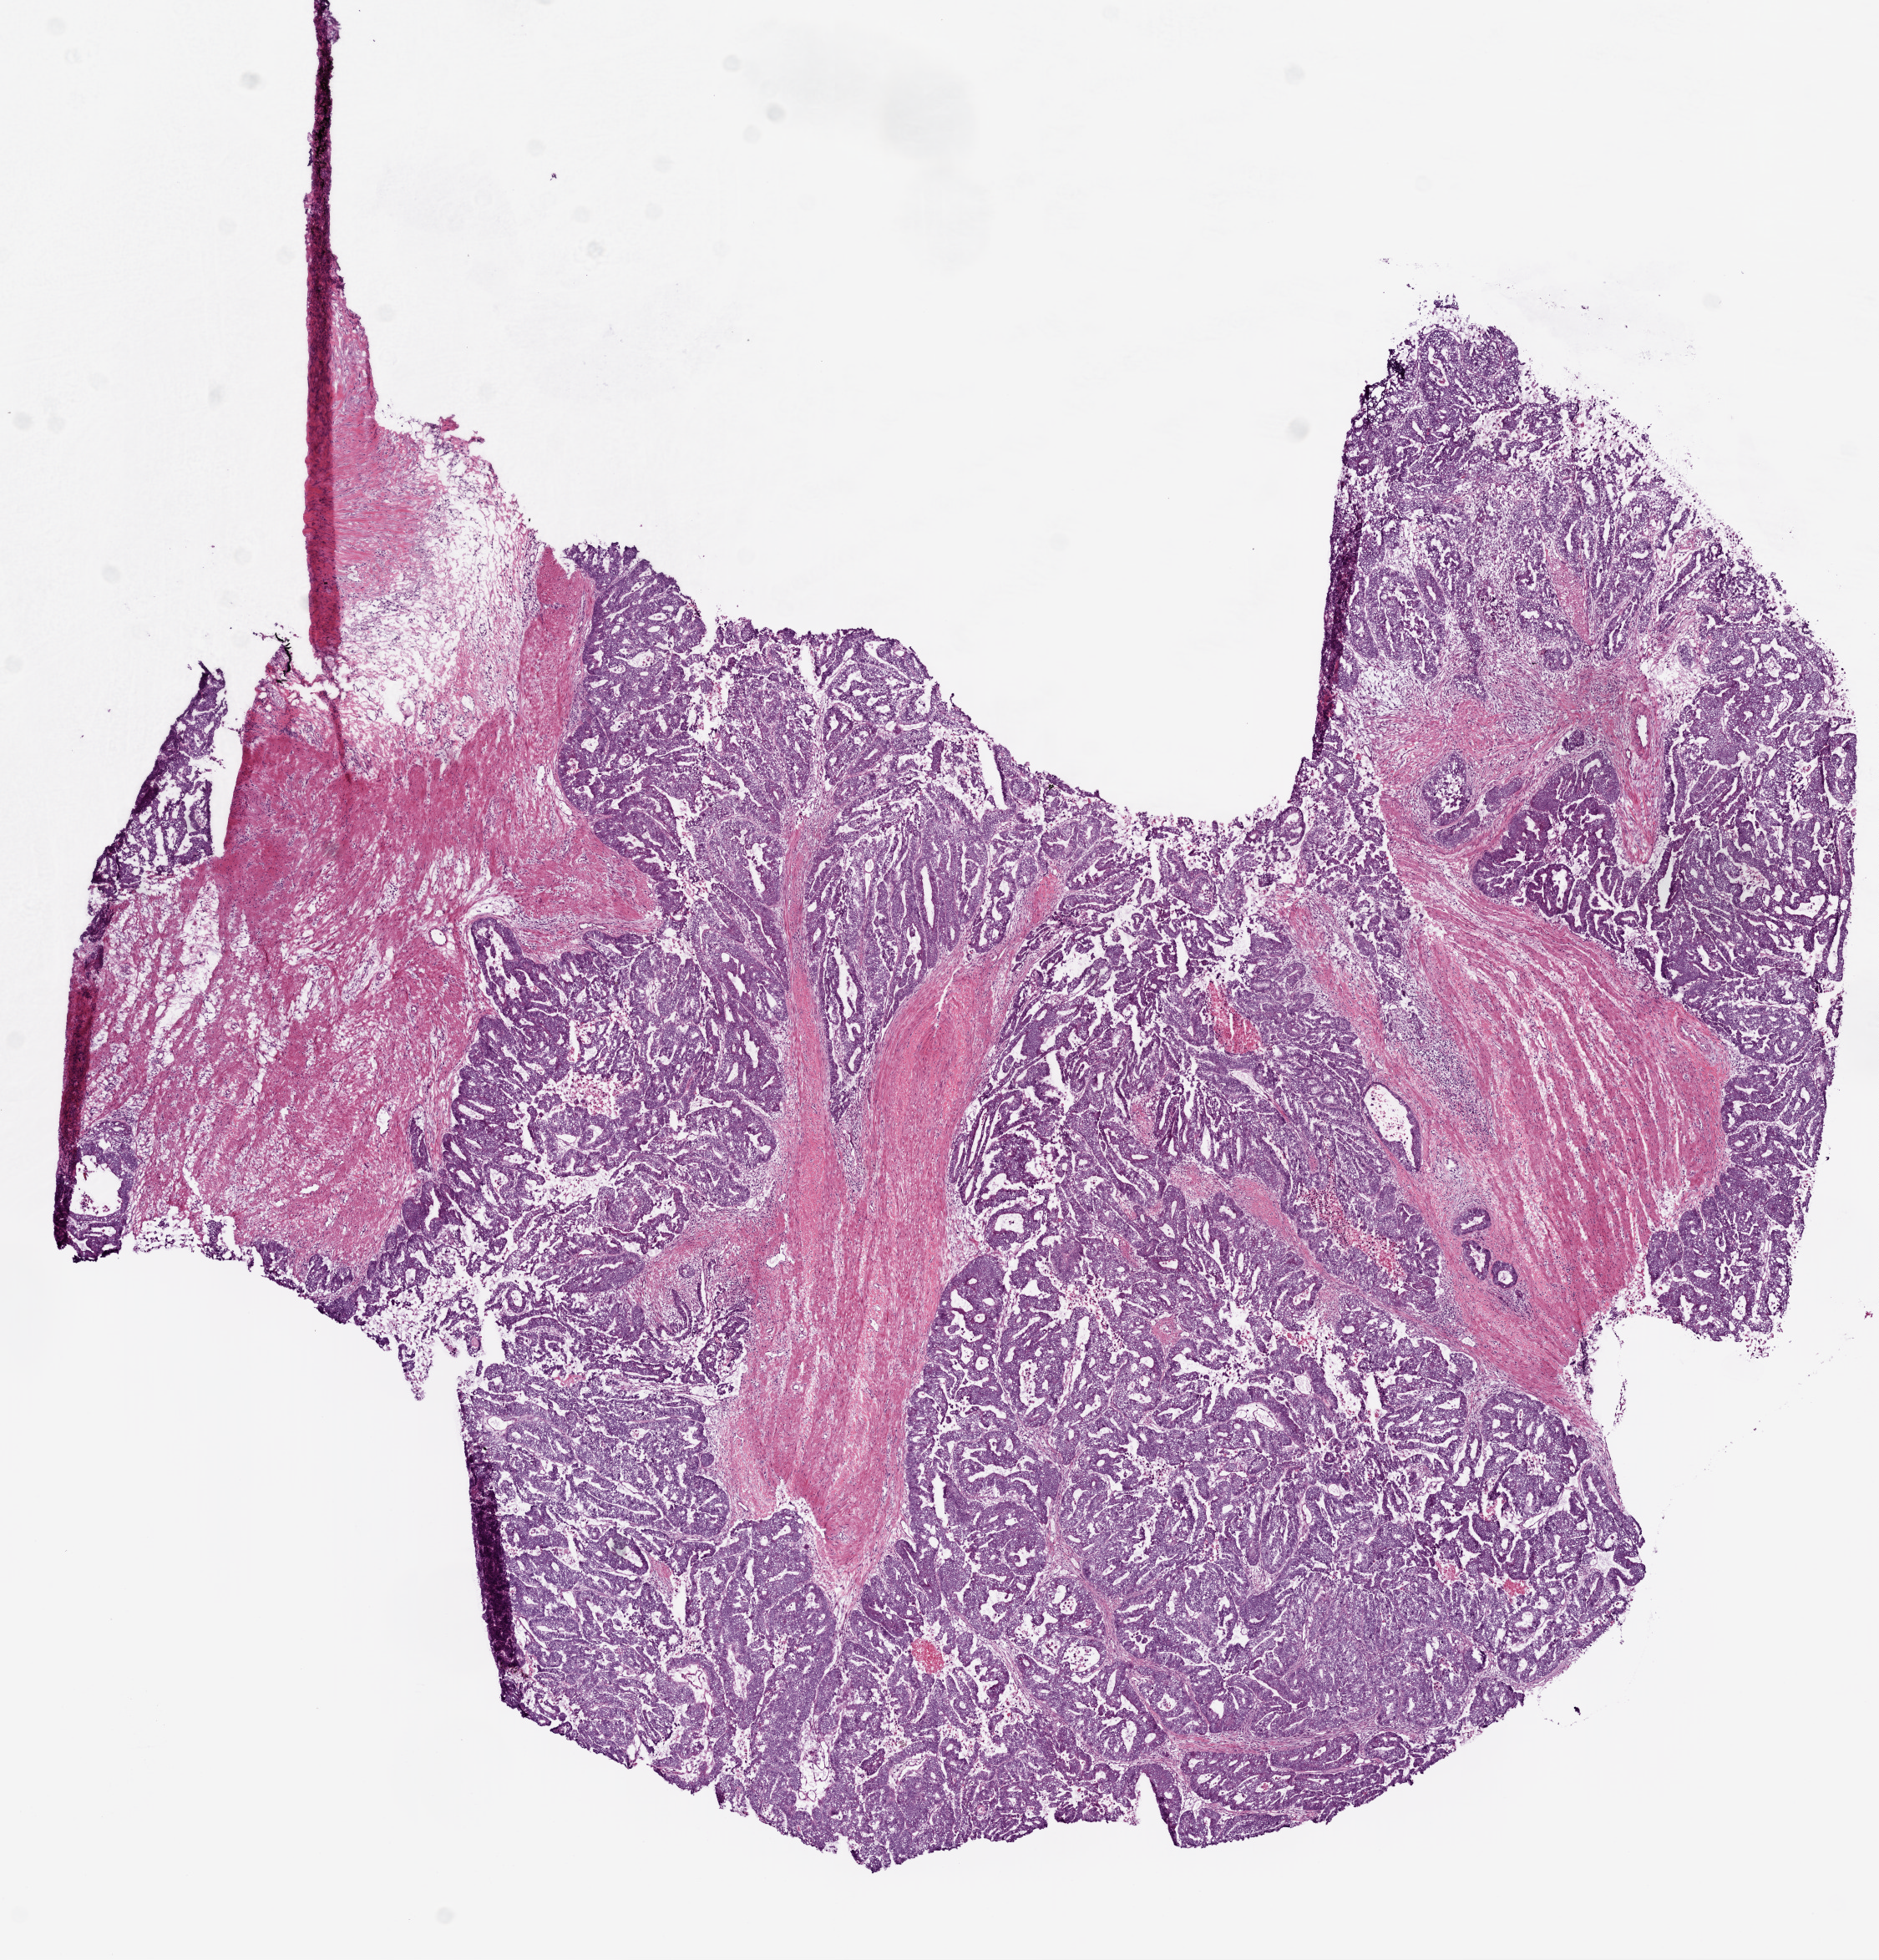
Hematoxylin and eosin (H&E) stained whole-slide image — low-resolution overview of the scanned area, about 9.0 x 9.4 mm. Frozen section from the bottom of the tissue portion. Primary tumour sample from the colon. Patient: male, age at initial diagnosis 82 years.
Diagnosis: Adenocarcinoma, NOS (ascending colon).